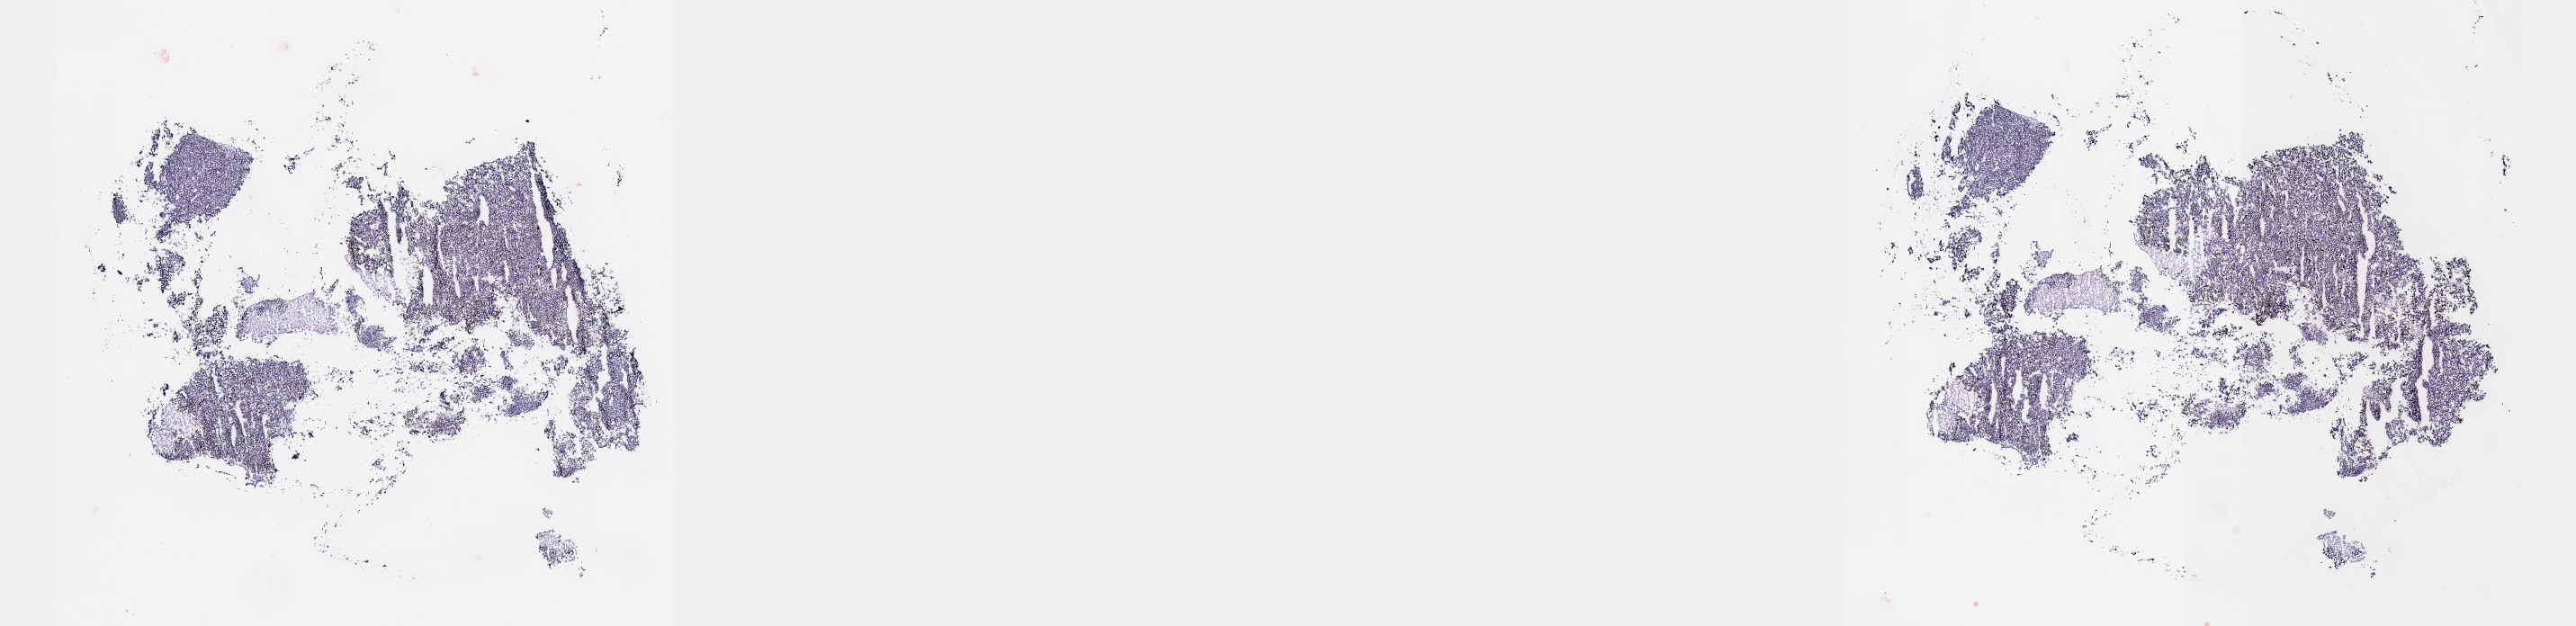
Whole-slide histology image, H&E — low-resolution overview of the scanned area, about 23.1 x 5.6 mm (from a 40x scan), frozen section from the top of the tissue portion, primary tumour sample from the uvea. Male, age 60 years at initial diagnosis. Composition of this section per pathologist review: tumour cells 90%, tumour nuclei 97%, normal cells 0%, stromal cells 0%, necrosis 10%. Inflammatory infiltration, as recorded: lymphocyte infiltration 0%, monocyte infiltration 0%, neutrophil infiltration 0%.
* laterality: left
* diagnosis: Spindle cell melanoma, type B (choroid)
* AJCC pathologic stage: IIA (7th edition)